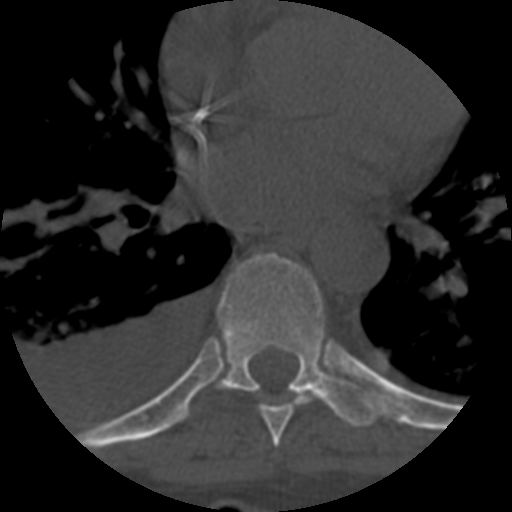
CT including the spine, one axial slice. Slice 404 of 708 in the series (ordered by position). Reconstruction kernel STANDARD. 120 kVp. One of 3 acquisitions stored at this slice position. Bone window (W 1800 / L 400 HU). 512 × 512 image matrix, field of view 160 × 160 mm. Patient age 55 years. From the clinical record (not read from this slice): primary cancer: colon; vertebrae with lytic lesions (as recorded): T12, L1, L5.
Structures marked on this image (semi-automatically segmented with operator editing):
- T7 vertebra: box from (x=258, y=391) to (x=317, y=448) px
- T8 vertebra: (x=215, y=253)–(x=379, y=427)